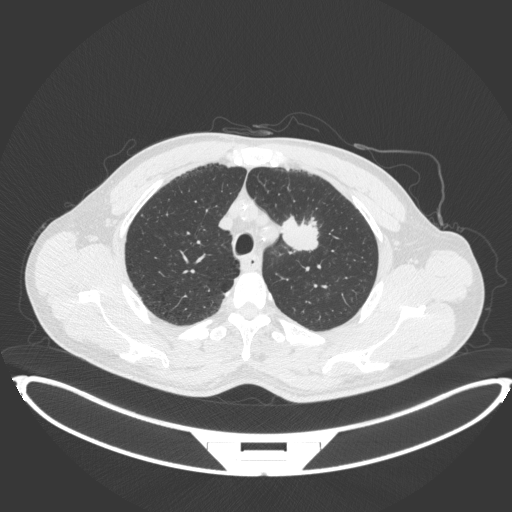
Chest CT, one axial slice; slice 344 of 407 in the series (ordered by position); reconstruction kernel B31f; 120 kVp; lung window (W 1500 / L -600 HU); 512 × 512 image matrix, field of view 457 × 457 mm. Patient: male, 60 years. Case-level facts recorded for this patient, not image findings: clinical TNM (as recorded): T2a N0 M0; histopathological grade: G1-G2.
Annotated regions visible in this slice (bounding box drawn by a radiologist):
- lung tumour (recorded histology: squamous cell carcinoma): bounding box [x1, y1, x2, y2] px = [278, 212, 321, 255]